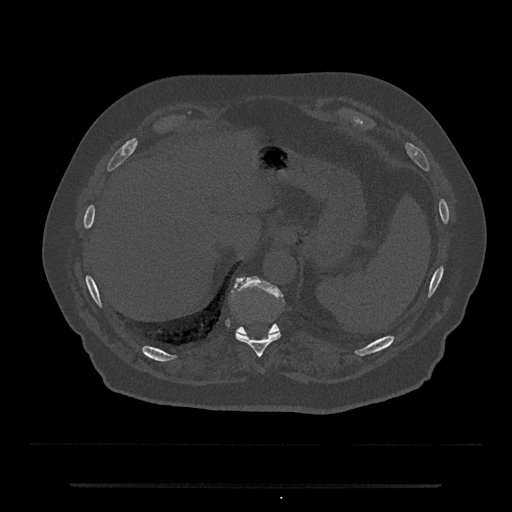
CT including the spine, one axial slice. Position 688 of 797 along the scan axis. Reconstruction kernel Br40s/3. Bone window (W 1800 / L 400 HU). 512 × 512 image matrix. Patient: male, 80 years. Case-level facts recorded for this patient, not image findings: primary cancer: prostate; vertebrae with lytic lesions (as recorded): L1, T11.
Structures marked on this image (semi-automatic segmentation, software-assisted and operator-edited):
- T10 vertebra: bounding box <235,332,281,357> (left, top, right, bottom; pixels)
- T11 vertebra: <232,276,283,335>